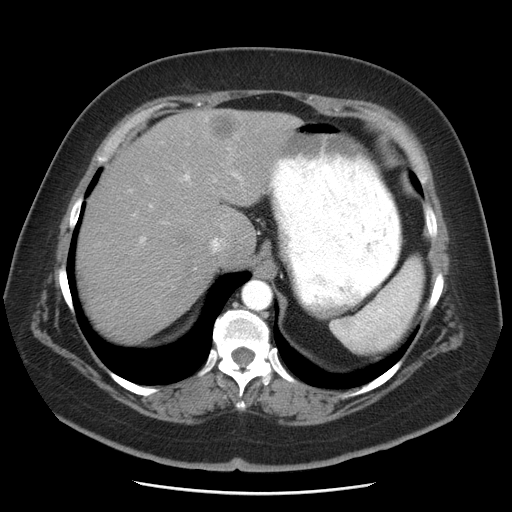
Contrast-enhanced abdominal CT, one axial slice; position 37 of 55 along the scan axis; intravenous contrast given; soft-tissue window (W 400 / L 40 HU); 5 mm slice thickness; 512 × 512 image matrix, field of view 380 × 380 mm. Female patient, age 52 years. Case-level facts recorded for this patient, not image findings: diagnosis: colorectal cancer liver metastases, imaged before liver resection; multiple liver metastases: yes; largest metastasis: 2.5 cm; disease in both lobes: yes.
Annotated regions visible in this slice (manually delineated by an expert):
- hepatic veins: bounding box [x1, y1, x2, y2] px = [210, 237, 225, 253]
- liver: [76, 108, 302, 345]
- planned liver remnant (the part of the liver to remain after resection): [76, 162, 214, 345]
- portal vein (with intrahepatic branches): [140, 147, 244, 242]
- liver metastasis: [205, 109, 245, 143]